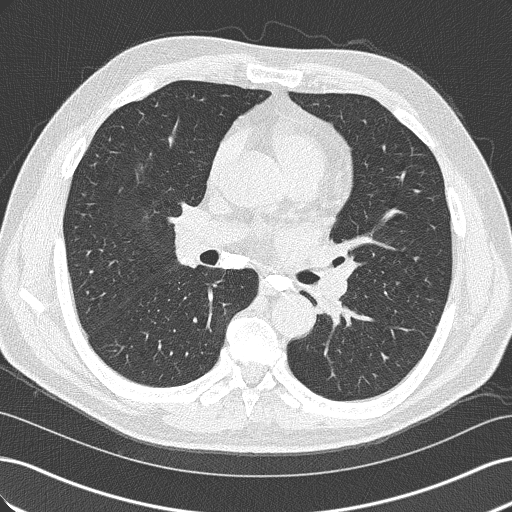
Low-dose screening chest CT, axial slice. Baseline screening round. Lung window (W 1500 / L -600 HU). 2 mm slice thickness. 512 × 512 image matrix, field of view 360 × 360 mm. Male participant, aged 57 years at enrolment. Former smoker at enrolment.
• Lesion marked by an expert reader, bounding box <301,285,360,341> (left, top, right, bottom; pixels).
• Screening reader's record for this exam: no non-calcified nodule ≥4 mm recorded.
• Official screen result: negative screen, minor abnormalities not suspicious for lung cancer.
• Lung cancer was diagnosed 363 days after this screen: squamous cell carcinoma, NOS, left lower lobe, moderately differentiated (G2), stage IIIB (AJCC 6th edition), 38 mm at pathology.